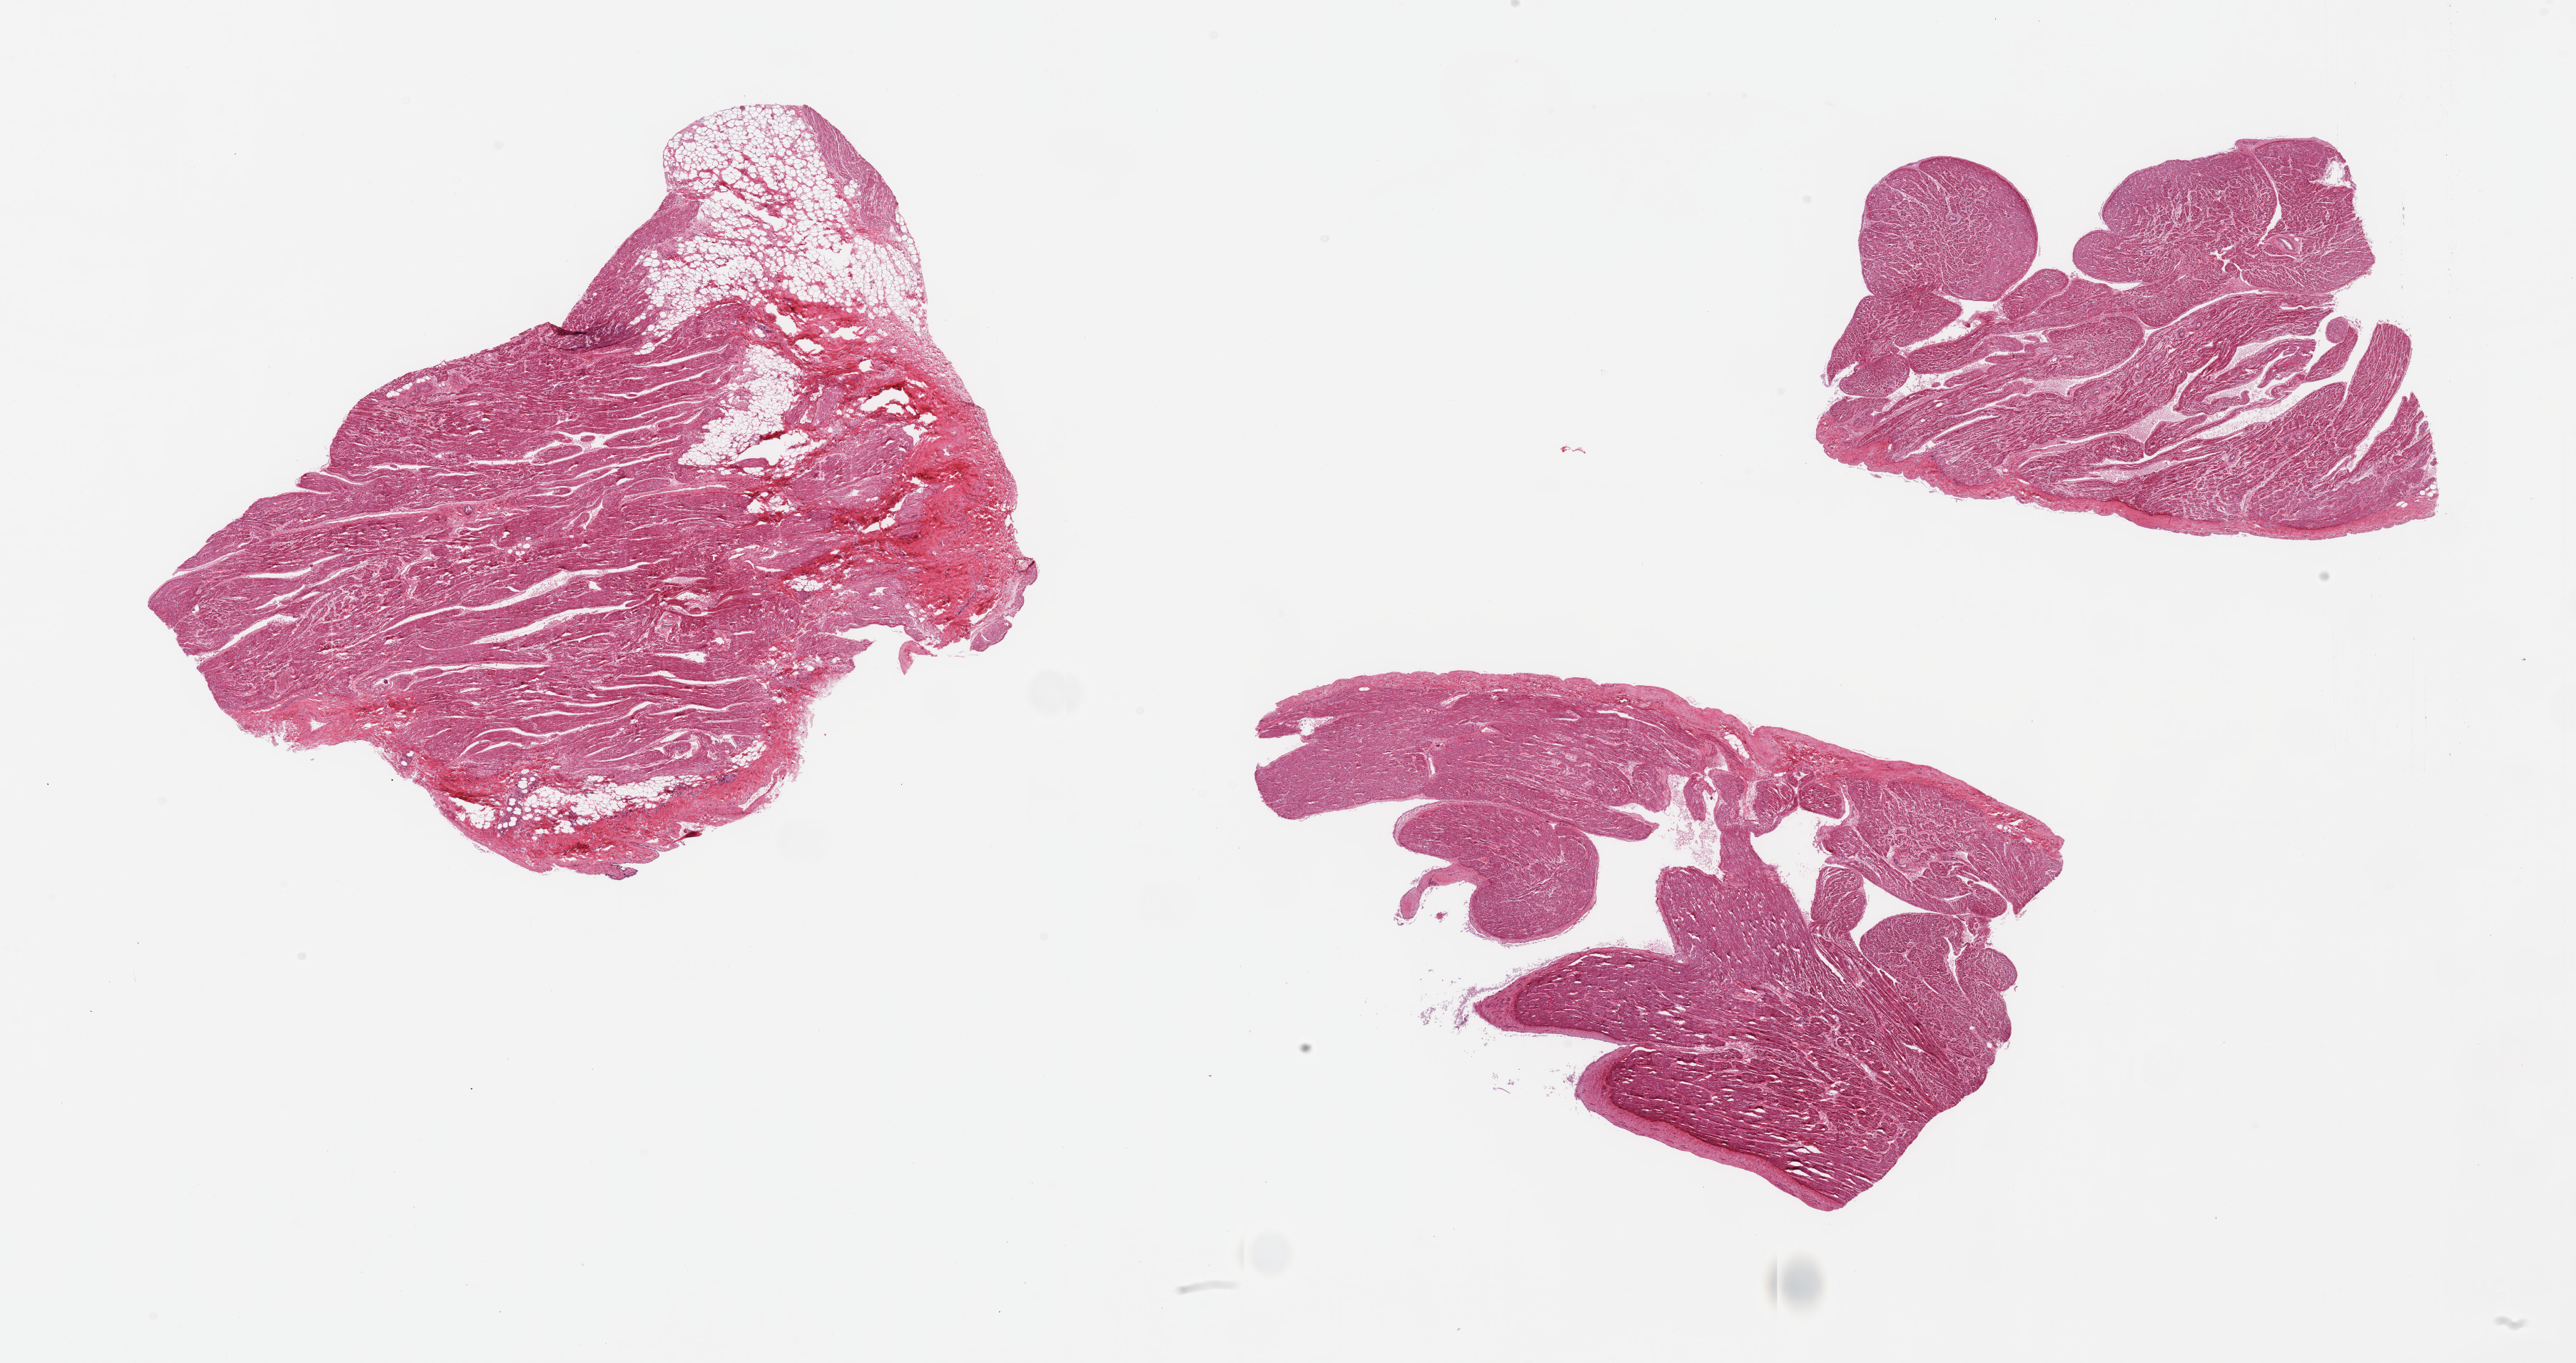
Haematoxylin and eosin whole-slide image, brightfield, low-resolution overview of the scanned area, about 28.5 x 15.1 mm (acquisition: 20x scan); PAXgene-fixed paraffin-embedded (PFPE) section; target tissue: auricular appendage; tissue donor sample. Donor: male.
Review note (as recorded): 3 pieces, no abnormalities.